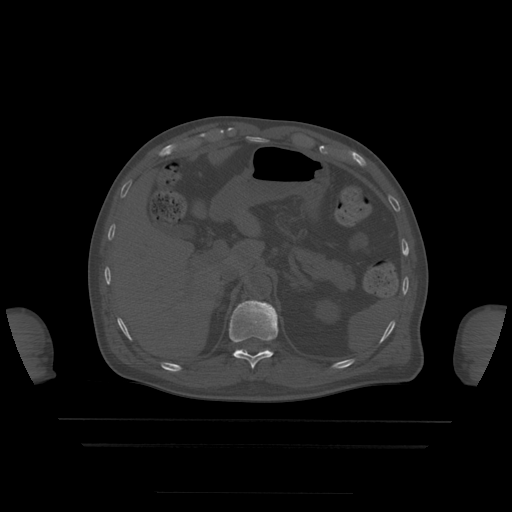
CT including the spine, one axial slice. Position 215 of 522 along the scan axis. Bone window (W 1800 / L 400 HU). 512 × 512 image matrix, field of view 436 × 436 mm. Patient age 68 years. Case-level facts recorded for this patient, not image findings: primary cancer: urothelial.
Outlined on this slice (semi-automatically segmented with operator editing):
- T11 vertebra: bounding box <229,300,279,369> (left, top, right, bottom; pixels)